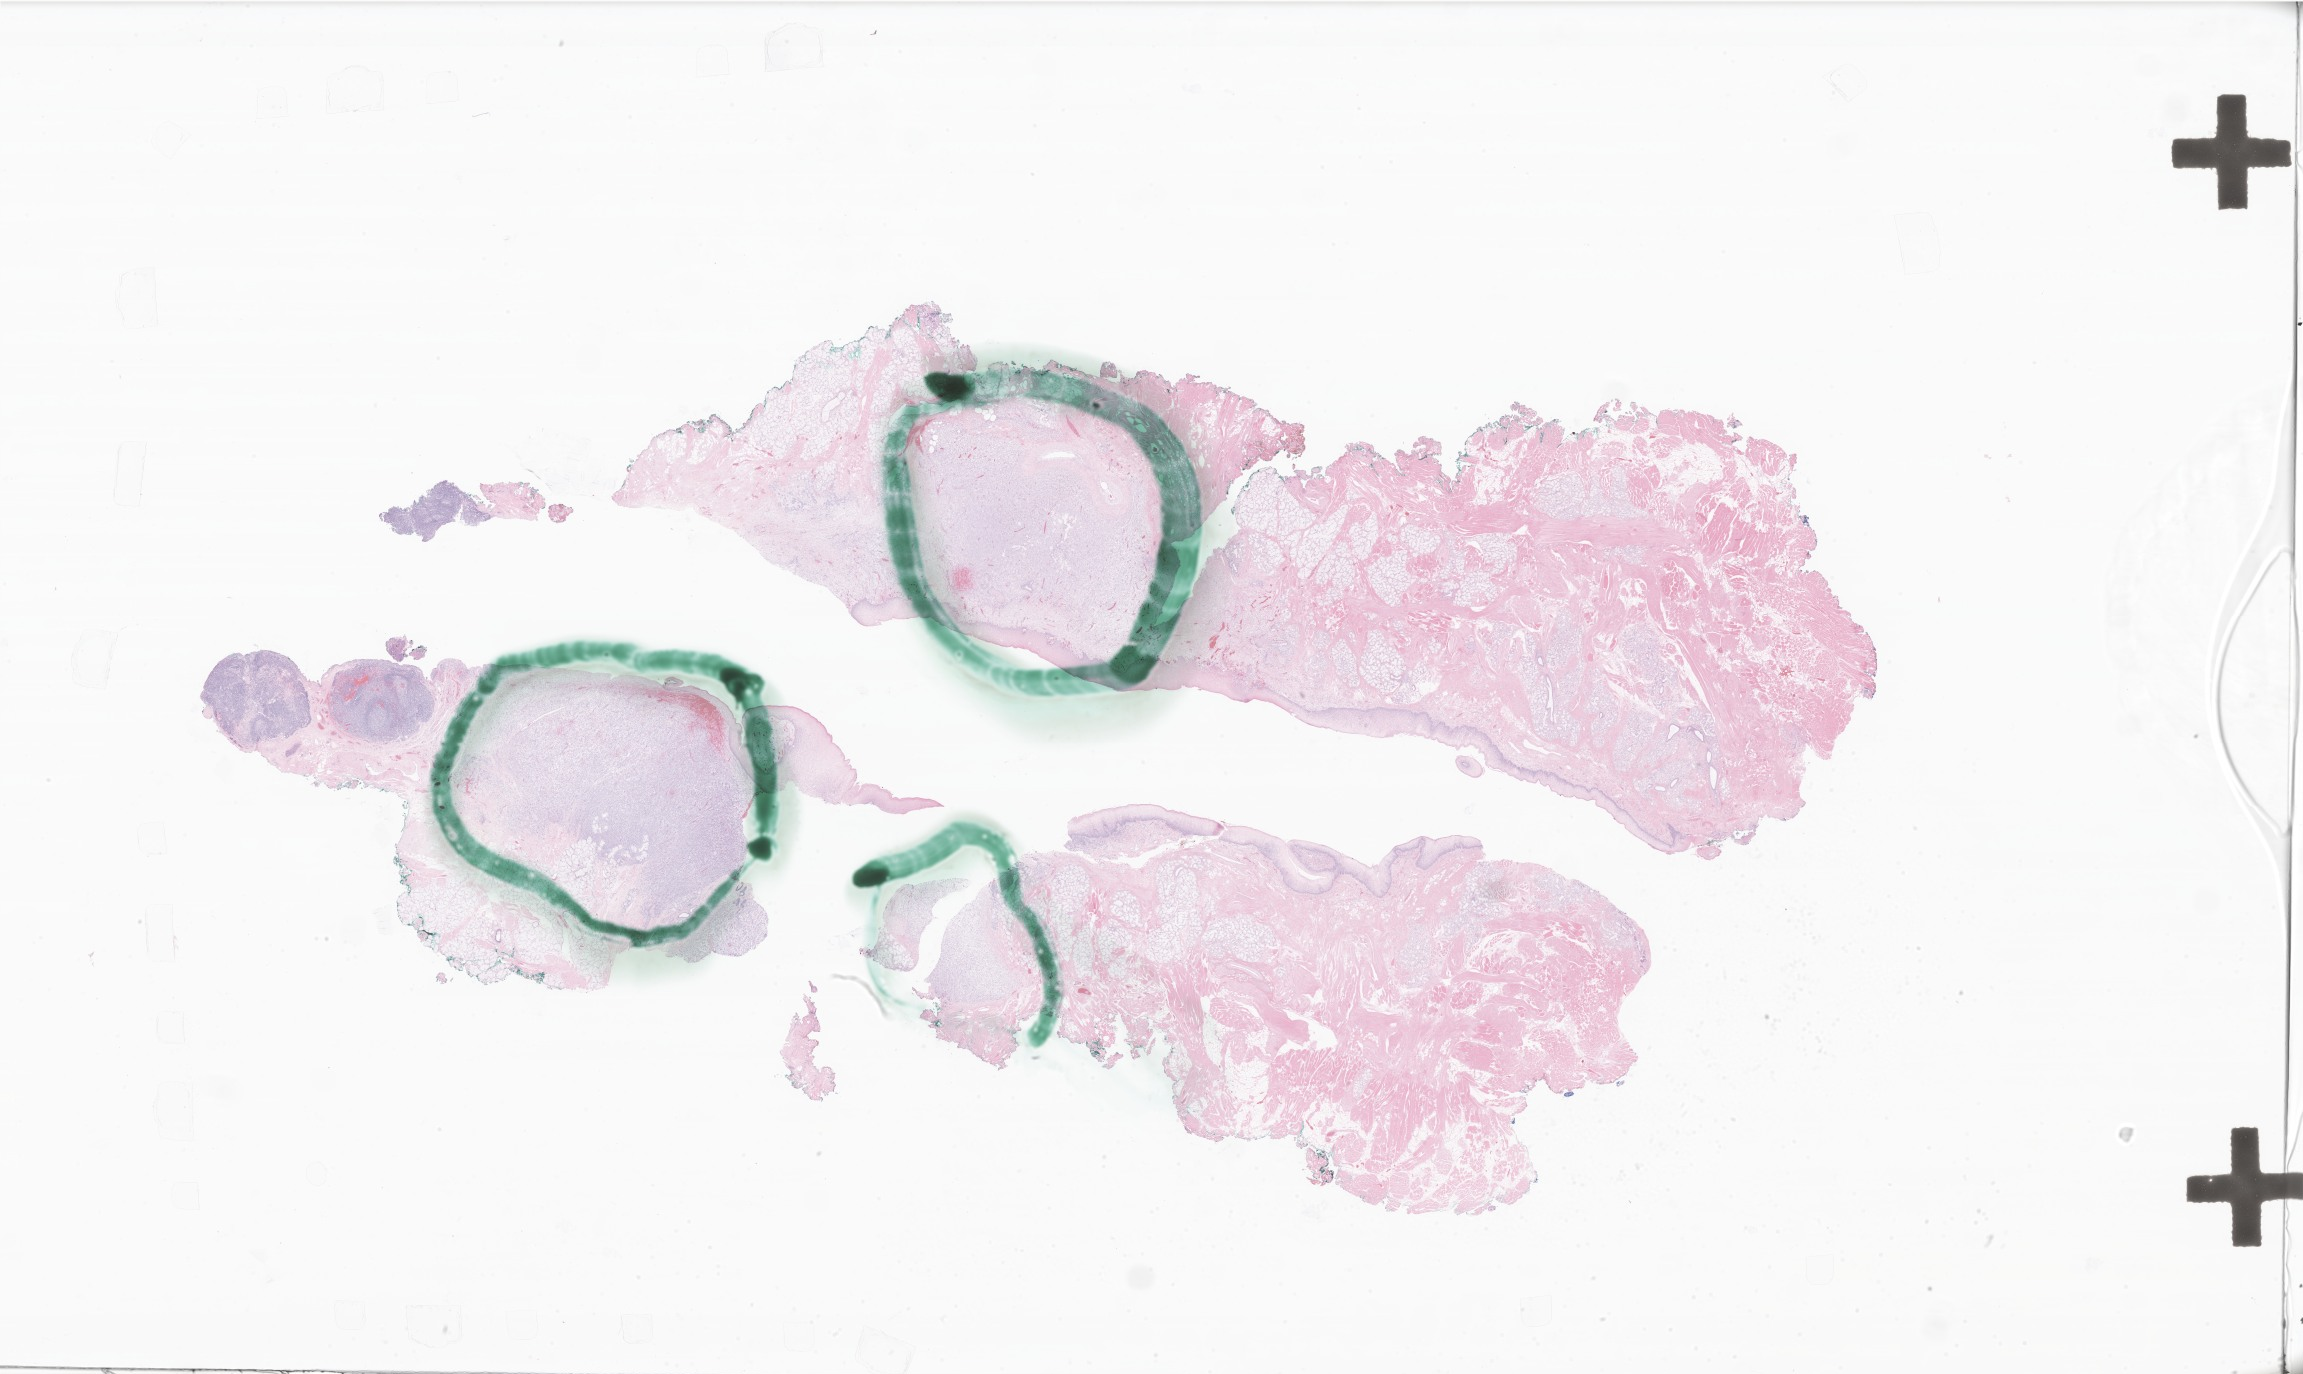
Hematoxylin and eosin (H&E) whole-slide image of tumor tissue from the root of tongue — whole scanned area (about 38.8 x 23.2 mm) shown as a low-resolution overview; FFPE section. Male patient, age 198 months (16 years 6 months).
Diagnosis (ICD-O-3 morphology term): Sarcoma, NOS. Tissue or organ of origin (case record): base of tongue.